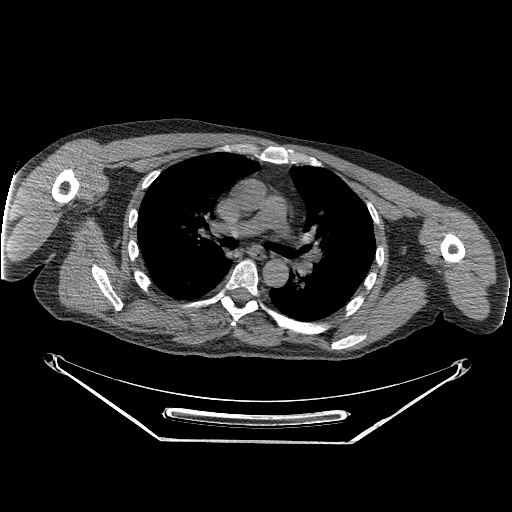
CT of an extremity soft-tissue mass (from a PET/CT study), one axial slice. Position 179 of 267 along the scan axis. Soft-tissue window (W 400 / L 40 HU). 3.75 mm slice thickness. 512 × 512 image matrix, field of view 500 × 500 mm. Male patient. From the clinical record (not read from this slice): histological type: pleiomorphic spindle cell undifferentiated; grade: high; site of the primary tumour: right parascapusular.
Annotated regions visible in this slice (expert contour drawn on MRI and transferred to this co-registered scan by the dataset authors):
- gross tumour volume including surrounding oedema: box from (x=94, y=292) to (x=223, y=334) px
- gross tumour volume (mass): (x=125, y=295)–(x=159, y=318)